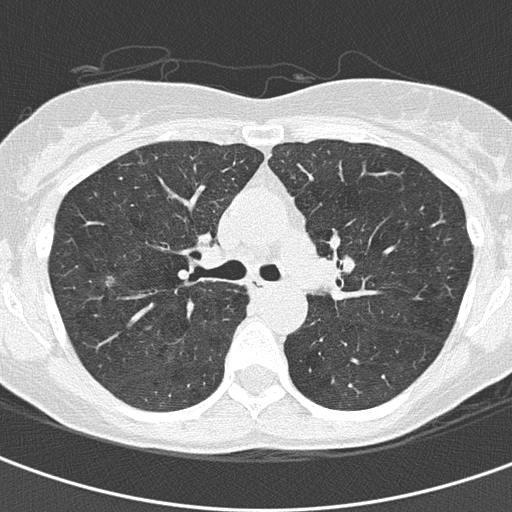
Low-dose screening chest CT, axial slice. First (baseline) screen. Lung window (W 1500 / L -600 HU). 2 mm slice thickness. Slice 52 of 156 in the series. Female participant, aged 59 years at enrolment. Current smoker at enrolment.
Expert reader's lesion annotation, box from (x=86, y=263) to (x=131, y=303) px. No non-calcified nodule or mass ≥4 mm was recorded by the screening reader at this exam. Official screen result: negative screen, minor abnormalities not suspicious for lung cancer.